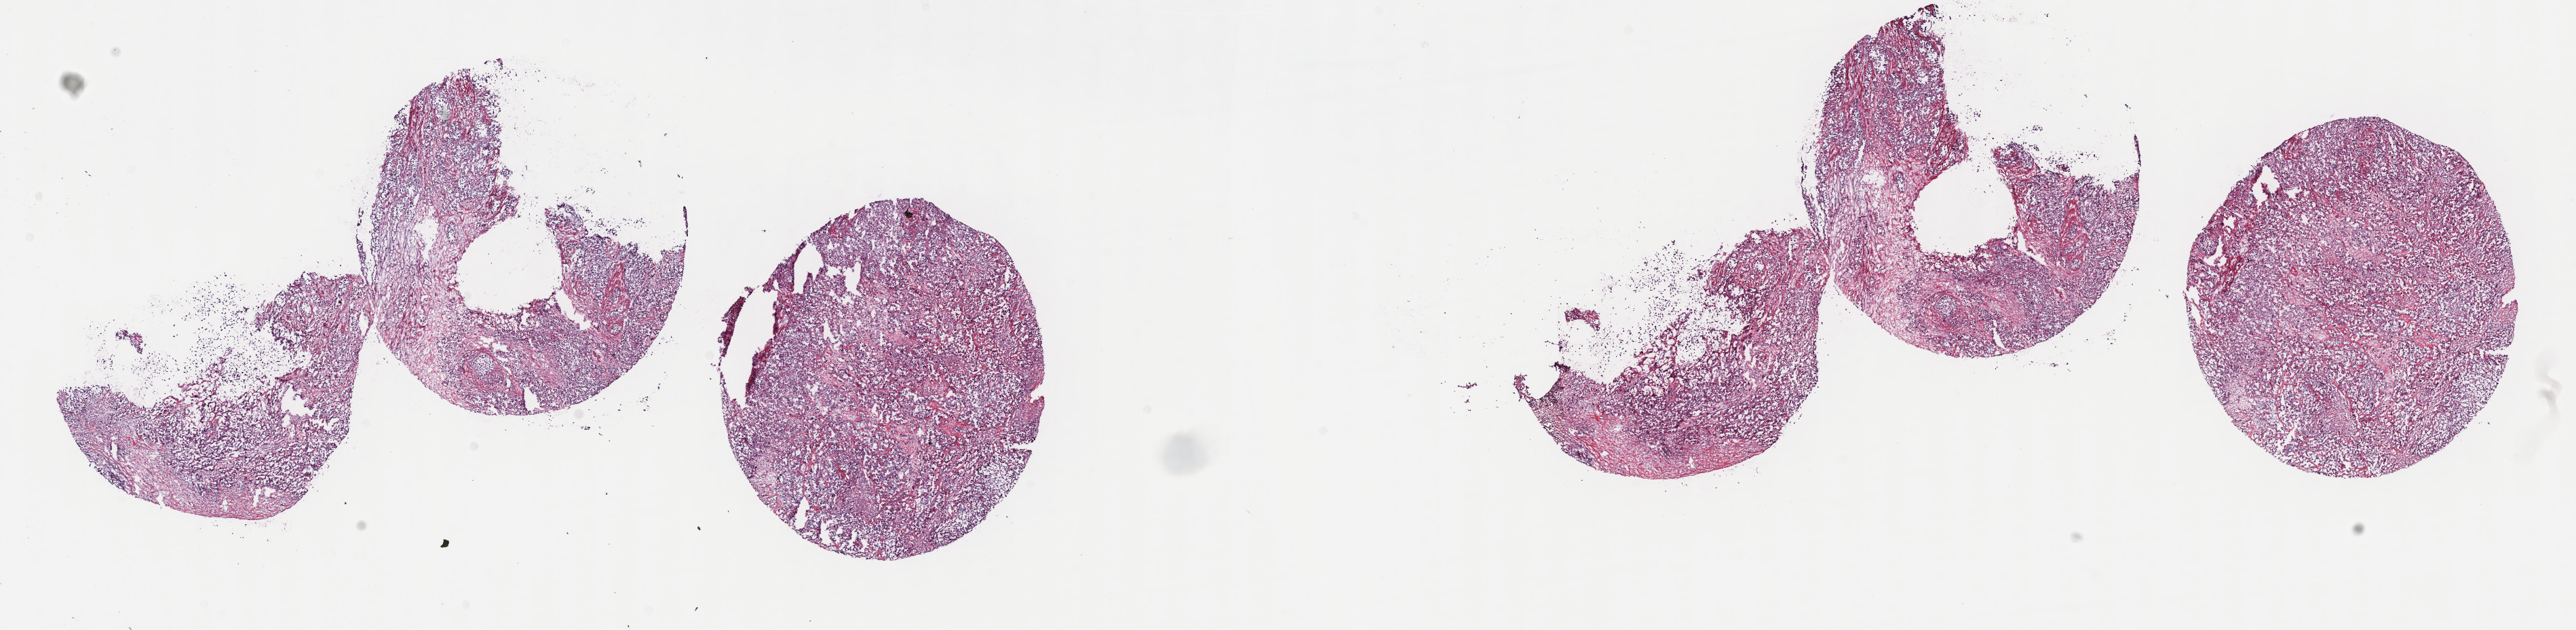
H&E whole-slide image, a low-resolution overview of the entire scanned area, about 30.7 x 7.5 mm, frozen section, sample: primary tumour, bladder. Female, age 73 years at initial diagnosis. Histologic grade: high grade. Pathologist review of this section (percent, as recorded): tumour cells 60%, tumour nuclei 60%, normal cells 0%, stromal cells 40%, necrosis 0%. Infiltration values recorded for this section: lymphocyte infiltration 0%, monocyte infiltration 0%, neutrophil infiltration 0%.
* histologic diagnosis: Transitional cell carcinoma
* AJCC pathologic stage: III (7th edition)
* lymph nodes positive (case pathology): 0 of 16 examined